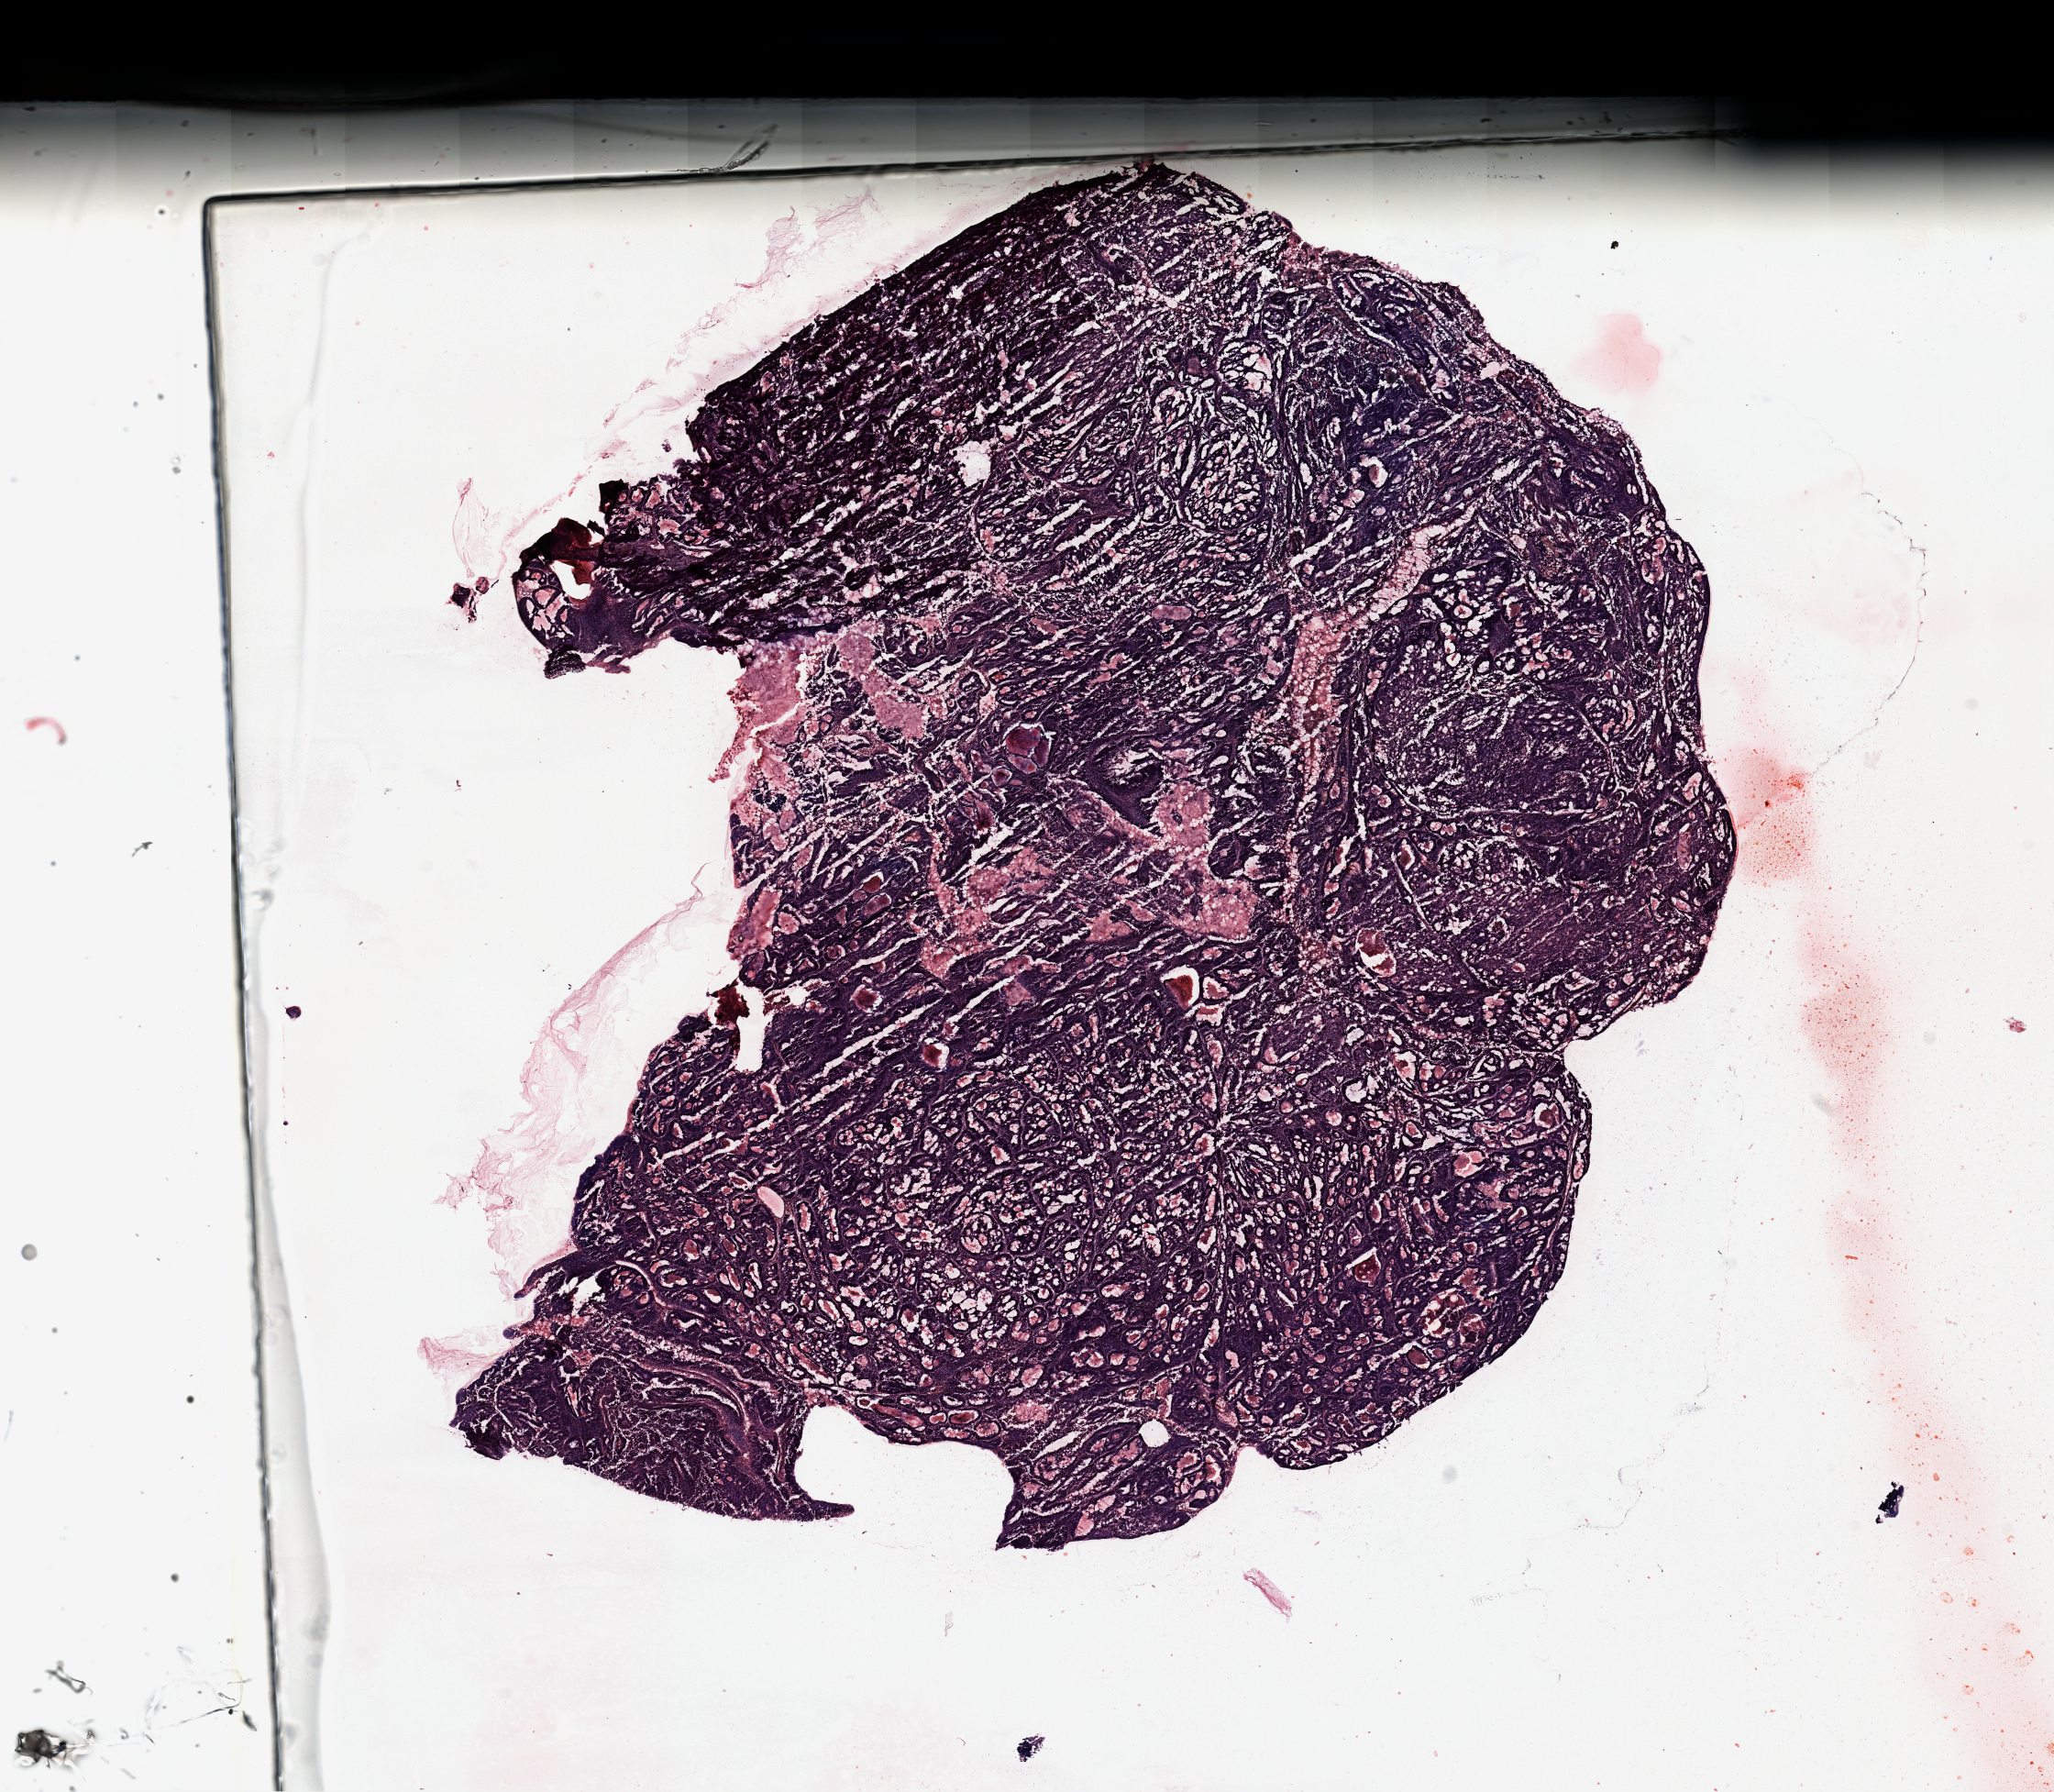
Whole-slide histology image, H&E-stained, shown as a low-resolution overview of the whole scanned area (about 17.7 x 15.5 mm, slide scanned at 20x). Tumour tissue sample, uterus. Patient: female, age 66 years. Histologic grade: G2 (moderately differentiated).
- AJCC pathologic stage: I
- diagnosis: Endometrioid adenocarcinoma, NOS